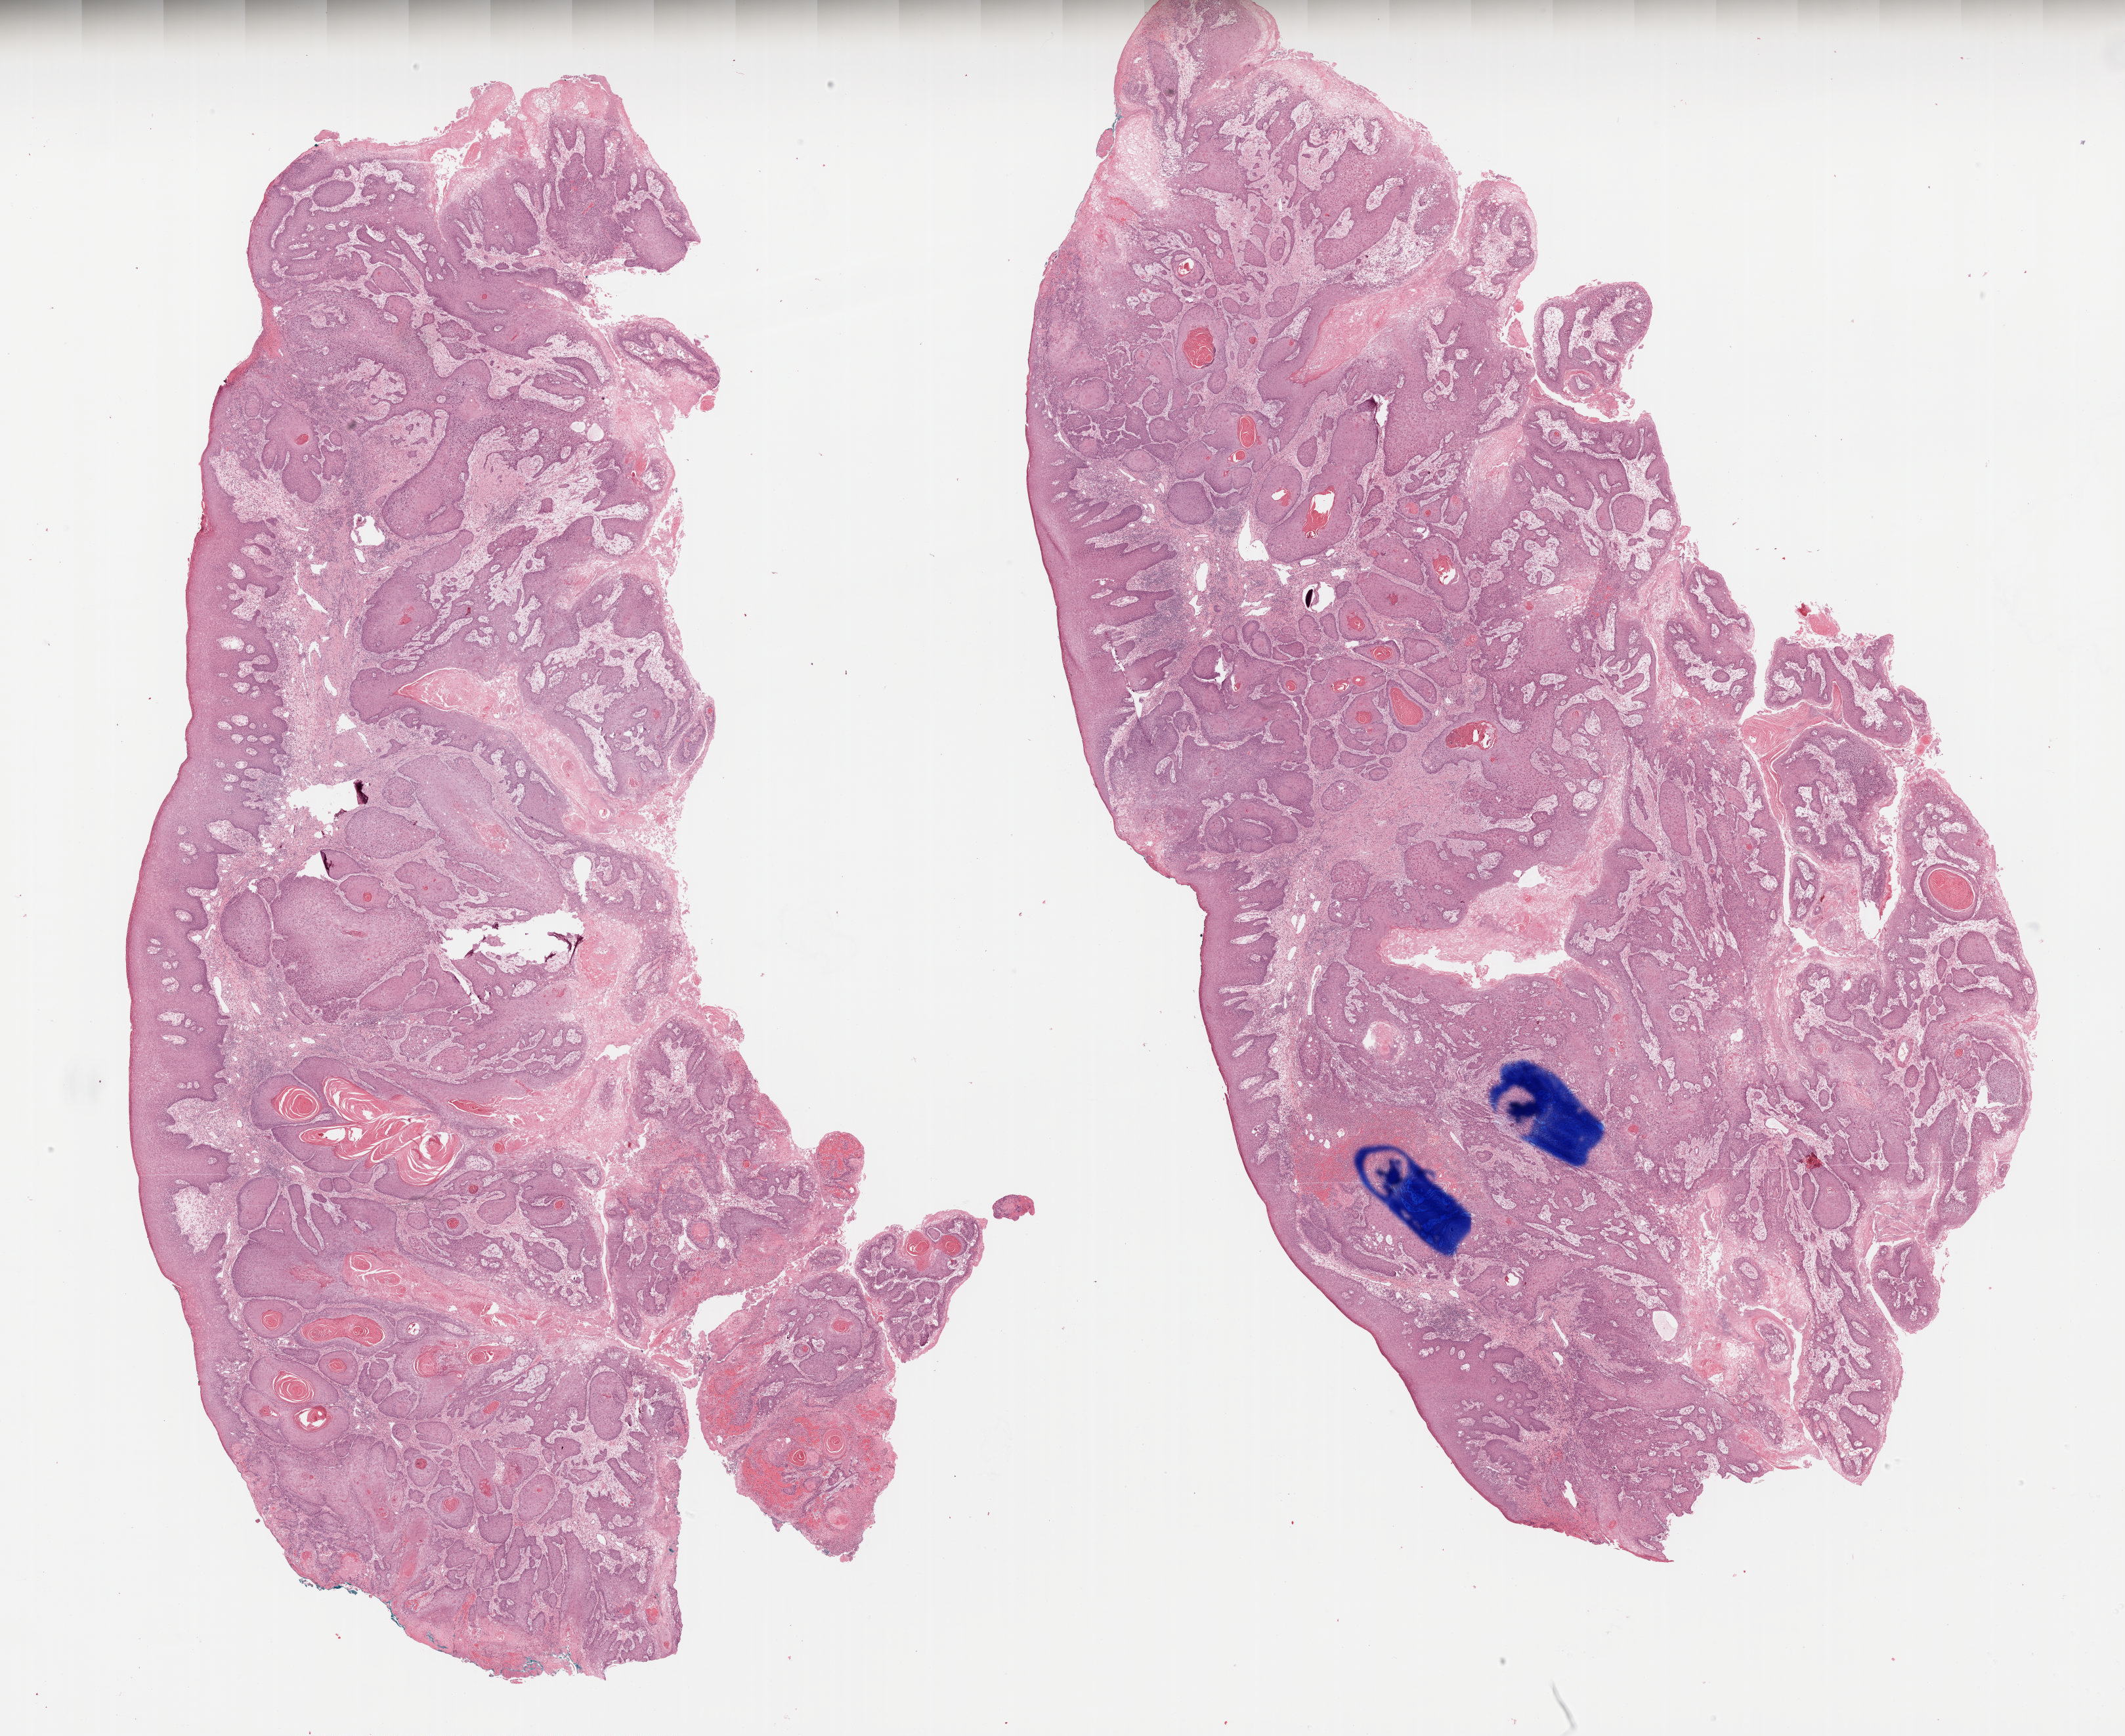
Digitized H&E tissue section (whole slide), shown as a low-resolution overview of the whole scanned area (about 26.0 x 21.2 mm), formalin-fixed paraffin-embedded (FFPE) diagnostic section, head and neck, primary tumour sample. Patient: male, age at initial diagnosis 58 years. Histologic grade: G2 (moderately differentiated).
* AJCC pathologic stage: II (7th edition)
* pathologic diagnosis: Squamous cell carcinoma, NOS
* lymph nodes positive (case pathology): 0 of 55 examined
* laterality: midline